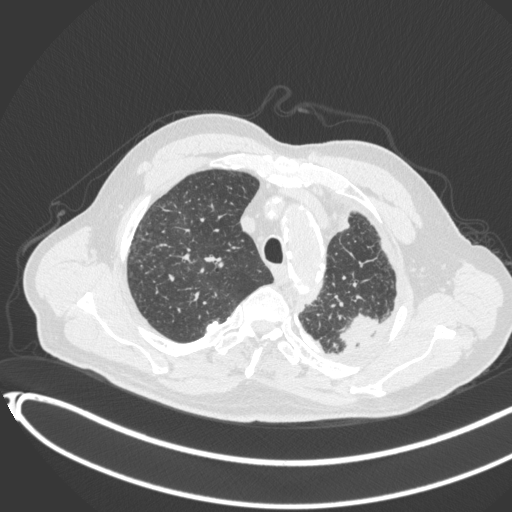
Chest CT, one axial slice. Slice 345 of 451 in the series (ordered by position). 120 kVp. Lung window (W 1500 / L -600 HU). 1 mm slice thickness. 512 × 512 image matrix, field of view 400 × 400 mm. Patient: male, 78 years. From the clinical record (not read from this slice): clinical TNM (as recorded): T1c N0 M1.
Structures marked on this image (rectangle marked by the reading radiologist):
- lung tumour (recorded histology: adenocarcinoma): box from (x=334, y=311) to (x=384, y=351) px